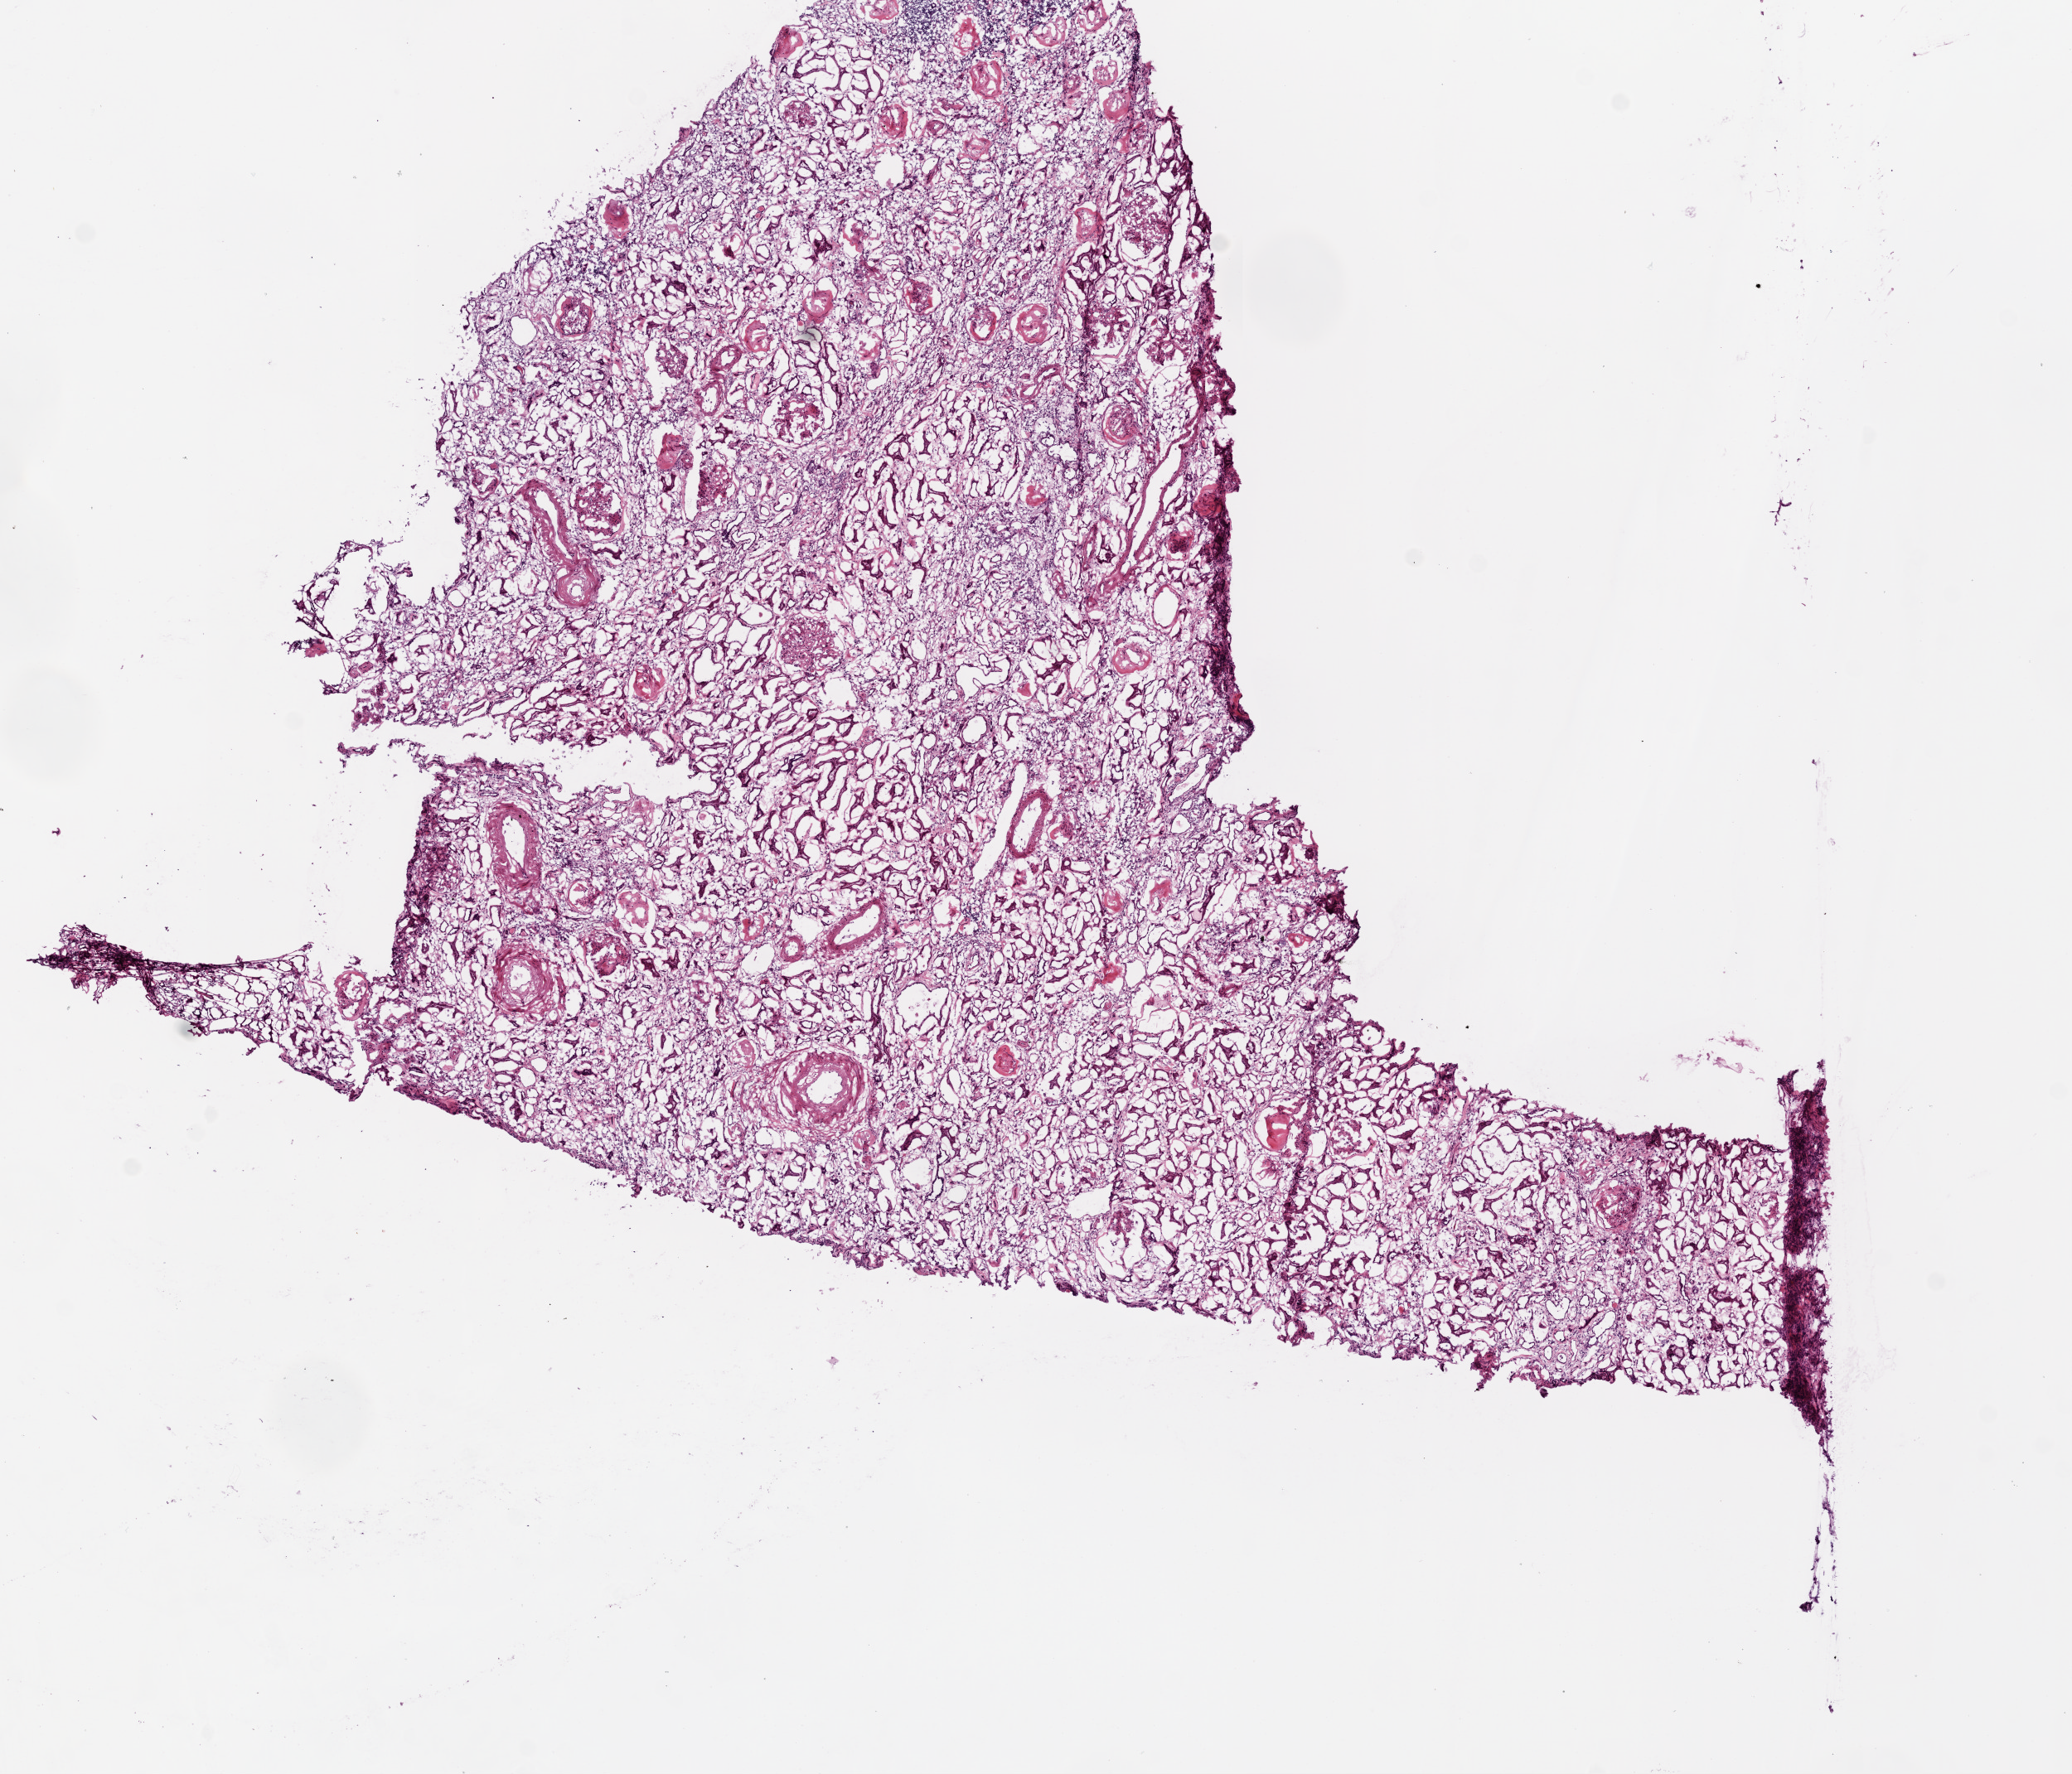
Whole-slide histology image, Hematoxylin and eosin (H&E) stained, shown as a low-resolution overview of the whole scanned area (about 10.0 x 8.6 mm). Frozen section from the top of the tissue portion. Sample: solid tissue normal (non-tumour tissue), kidney. Female patient; age at initial diagnosis 70 years.
This section: solid tissue normal sample (biorepository sample class). Patient diagnosis: Clear cell adenocarcinoma, NOS.